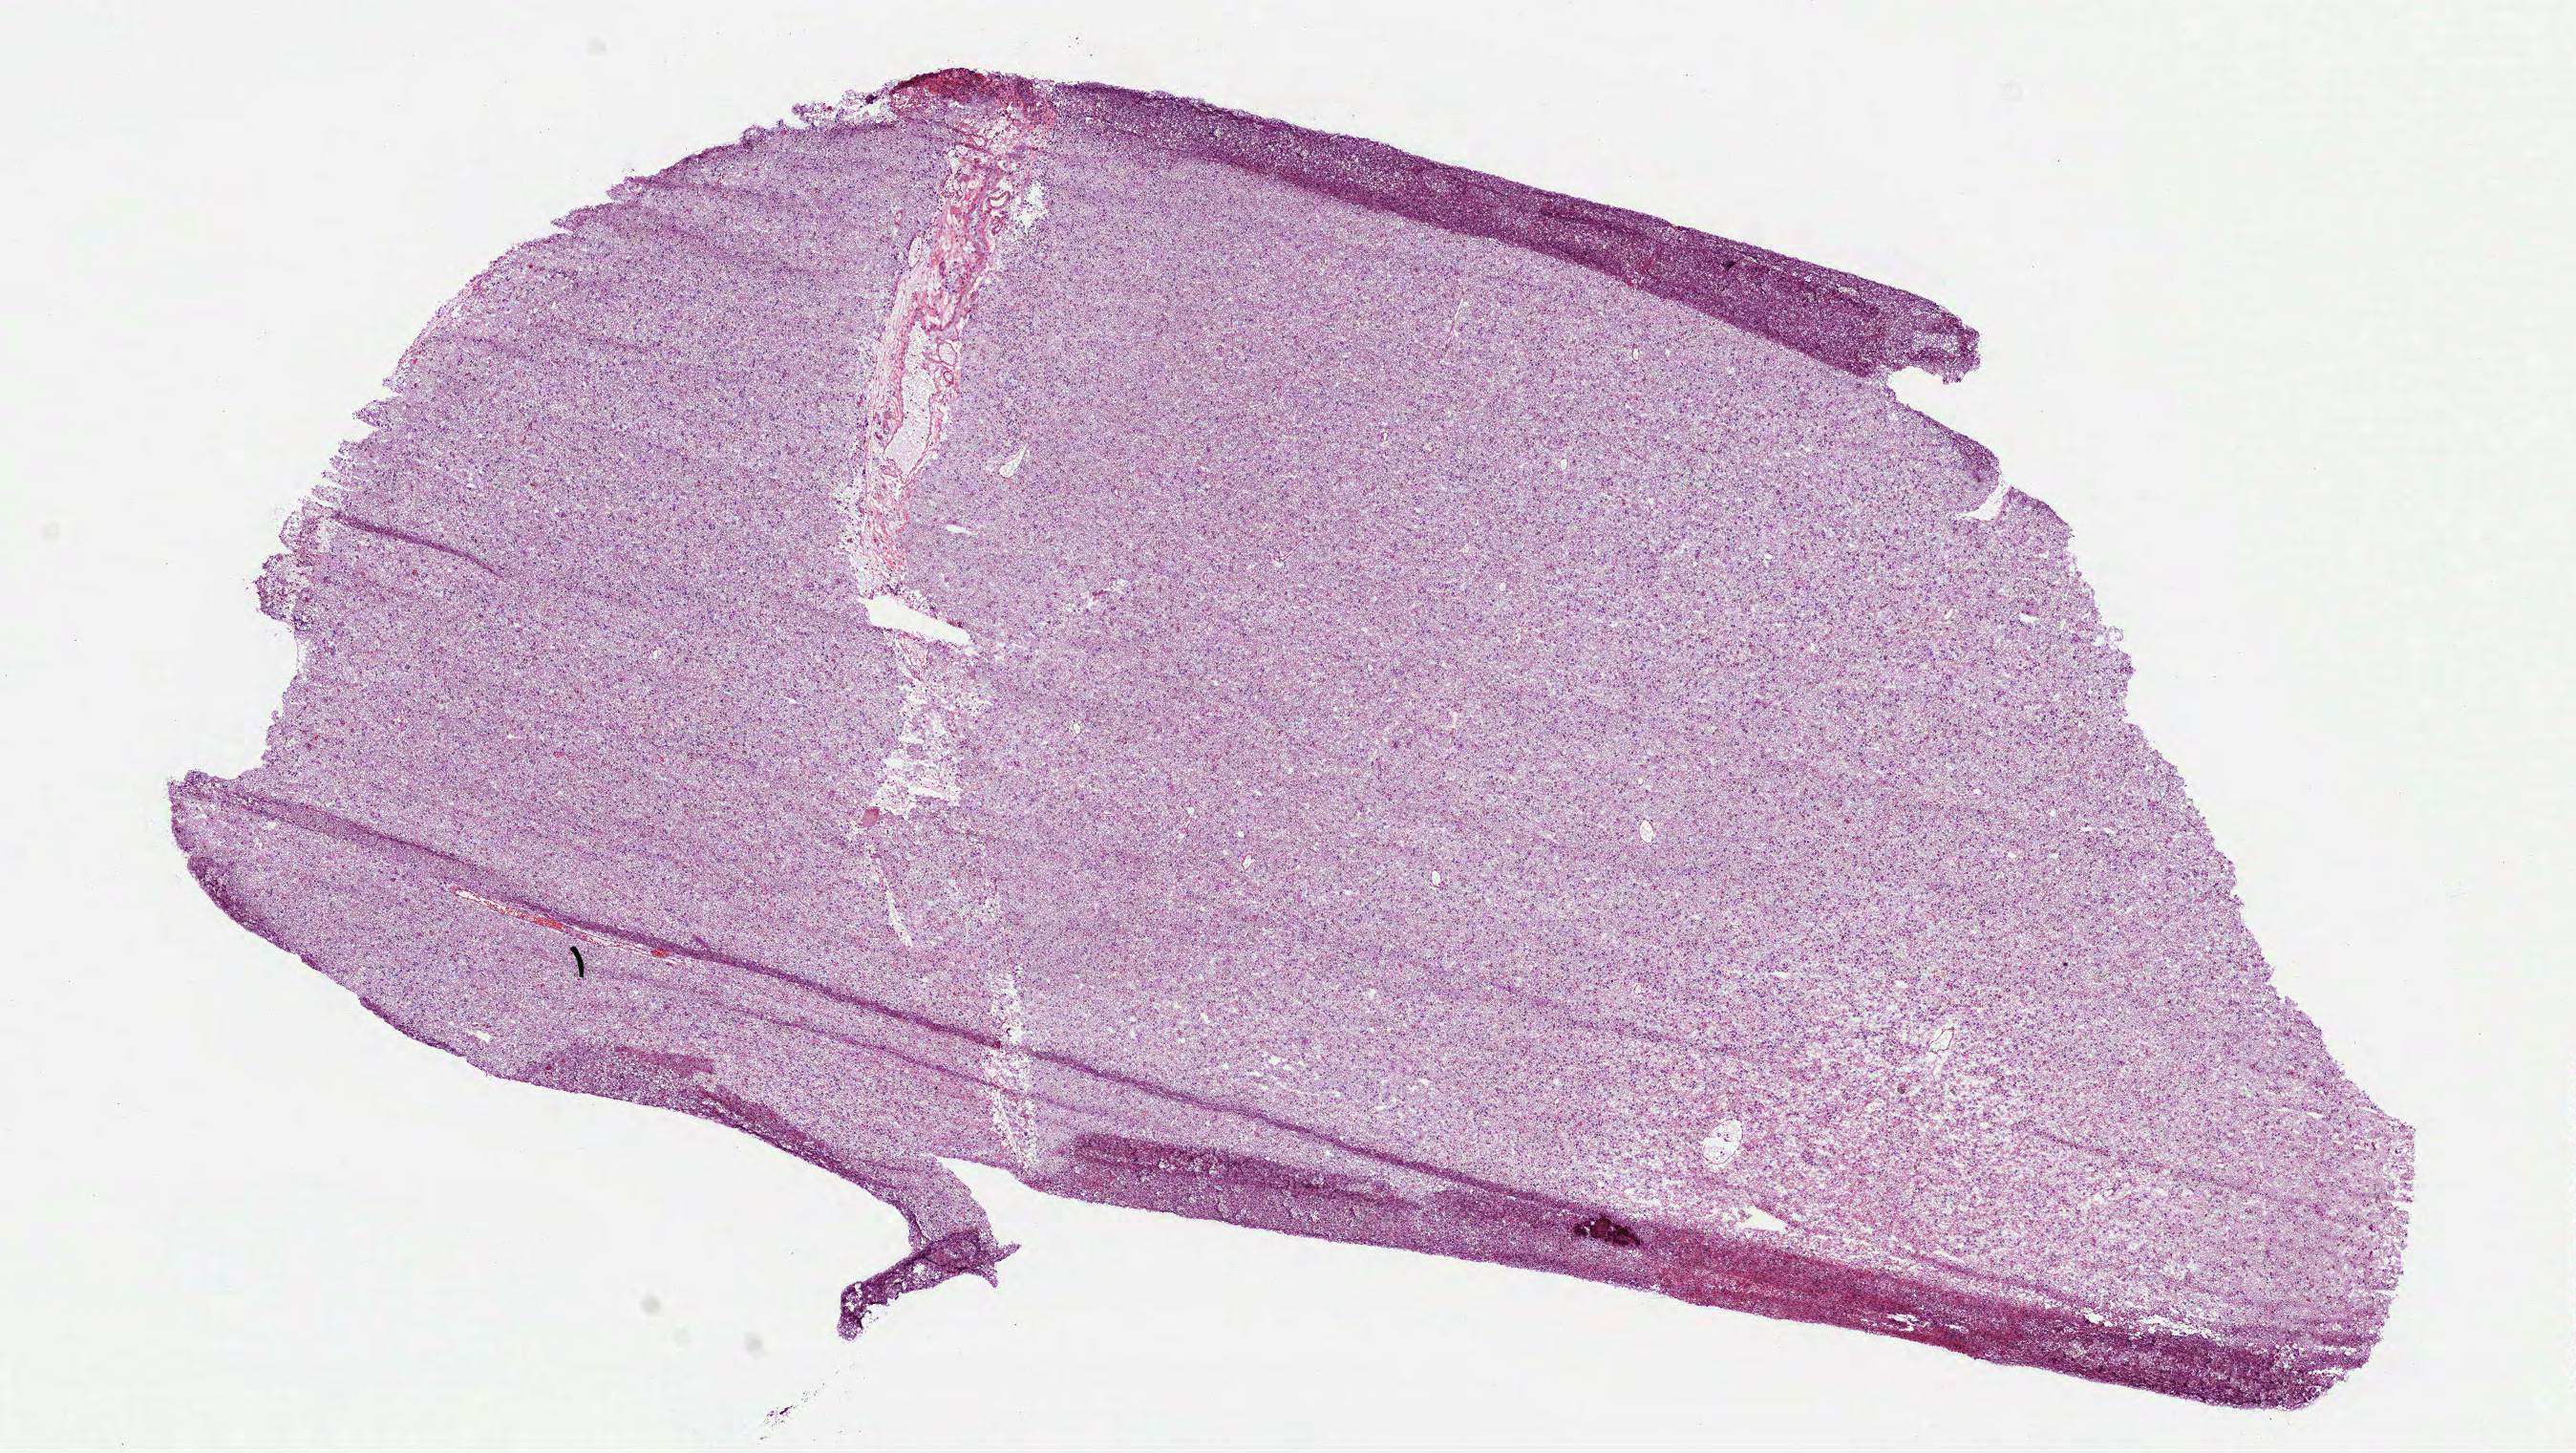
Hematoxylin and eosin (H&E) stained whole-slide image, a low-resolution overview of the entire scanned area, about 10.9 x 6.1 mm (acquisition: 40x scan), frozen section from the top of the tissue portion, primary tumour sample from the brain. Female, age 48 years at initial diagnosis. Histologic grade: G3 (poorly differentiated). Pathologist review of this section (percent, as recorded): tumour cells 100%, tumour nuclei 65%, normal cells 0%, stromal cells 0%, necrosis 0%.
- diagnosis: Oligodendroglioma, anaplastic (cerebrum)